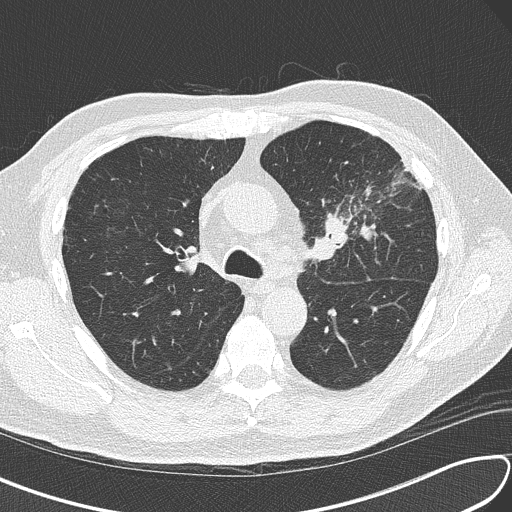
Low-dose screening chest CT, axial slice, third annual screen, lung window (W 1500 / L -600 HU), 2 mm slice thickness. Male, age 67 years at enrolment.
Expert-annotated lung lesion, box from (x=298, y=176) to (x=399, y=271) px. Screening reader's record for this exam (one nodule recorded; not confirmed to be the boxed lesion): non-calcified nodule or mass ≥4 mm, left upper lobe, 30 × 23 mm, soft tissue attenuation, pre-existing on the prior screen: no. Lung cancer was diagnosed 41 days after this screen: small cell carcinoma, NOS, left upper lobe, stage IV (AJCC 6th edition), 30 mm at pathology.